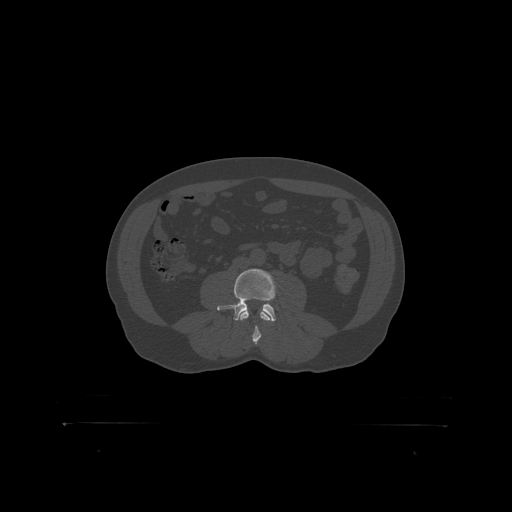
CT including the spine, one axial slice; position 248 of 399 along the scan axis; reconstruction kernel STANDARD; 120 kVp; bone window (W 1800 / L 400 HU); 1.25 mm slice thickness; 512 × 512 image matrix, field of view 650 × 650 mm. Patient: male, 46 years. Case-level facts recorded for this patient, not image findings: primary cancer: skin.
Structures marked on this image (semi-automatically segmented with operator editing):
- L3 vertebra: bounding box [x1, y1, x2, y2] px = [241, 311, 269, 319]
- L4 vertebra: [220, 270, 276, 317]